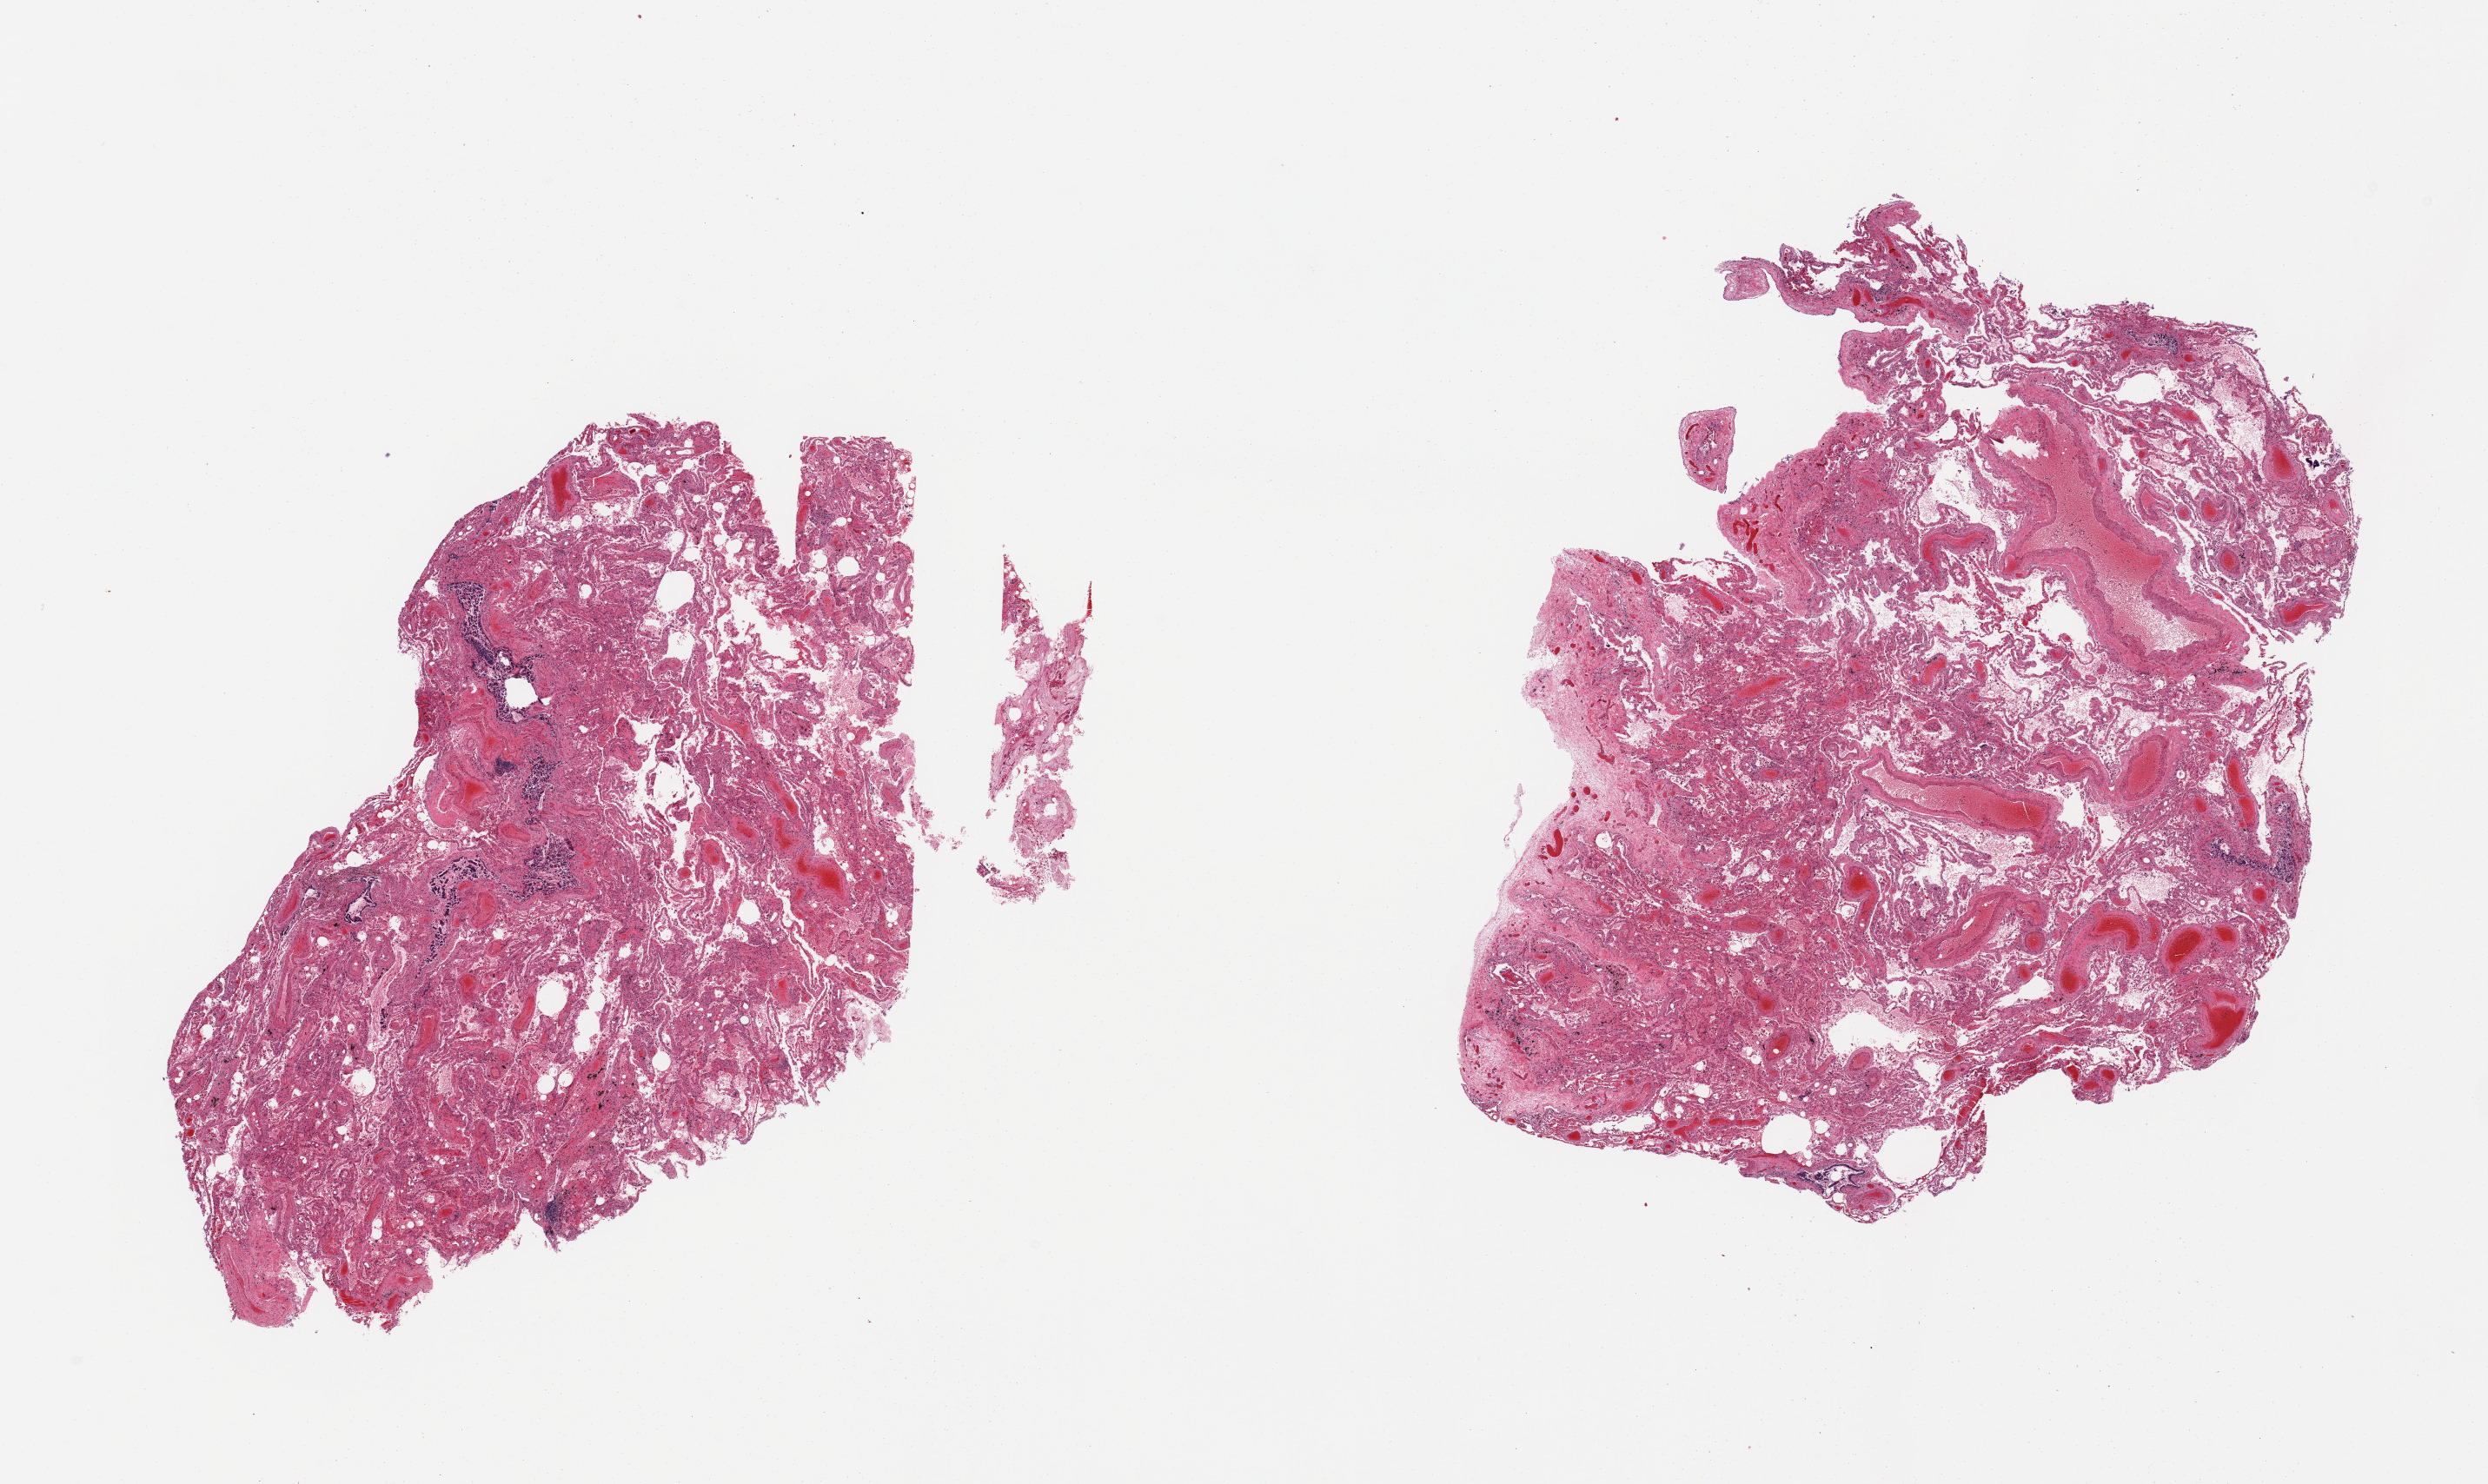
Digitized H&E-stained section — a low-resolution overview of the entire scanned area, about 22.6 x 13.5 mm, PAXgene-fixed paraffin-embedded (PFPE) section, target tissue: lung, tissue donor sample.
• pathologist's review note for this sample: 2 pieces, moderate congestion